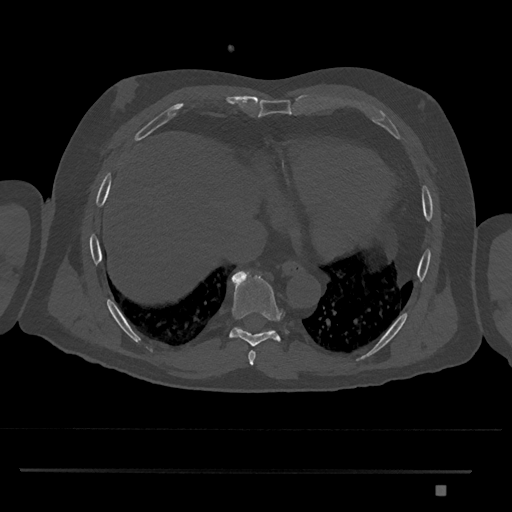
CT including the spine, one axial slice. Slice 1104 of 1134 in the series (ordered by position). Reconstruction kernel Br40s/3. 120 kVp. Bone window (W 1800 / L 400 HU). 0.5 mm slice thickness. 512 × 512 image matrix, field of view 429 × 429 mm. Patient: male, 65 years. From the clinical record (not read from this slice): primary cancer: prostate.
Structures marked on this image (semi-automatic segmentation, software-assisted and operator-edited):
- T8 vertebra: bounding box [x1, y1, x2, y2] px = [229, 270, 282, 346]
- T9 vertebra: [236, 327, 273, 332]